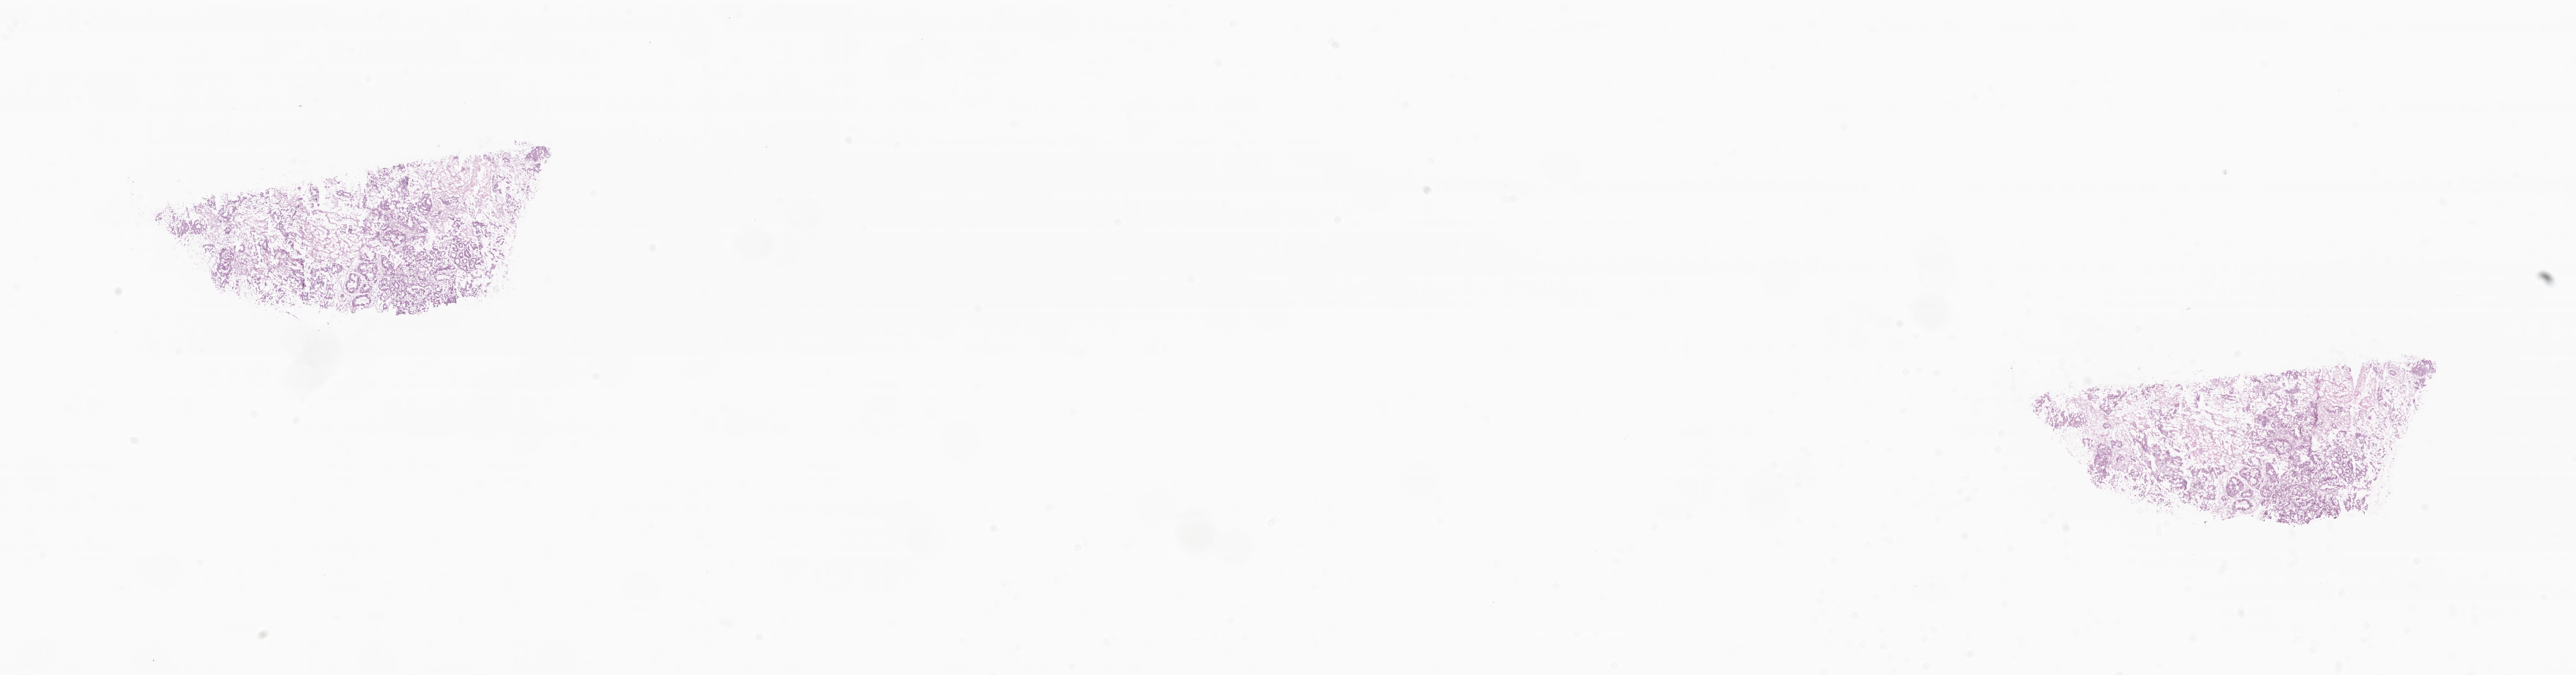
Whole-slide image, haematoxylin and eosin stain, low-resolution overview of the scanned area, about 34.0 x 8.9 mm, frozen section, primary tumor, anatomic site: rectum. Patient sex: male. Tumor grade: G2 (moderately differentiated). Composition of this section per pathologist review: tumor cells 100%, tumor nuclei 75%, stromal cells 0%, necrosis 0%, normal cells 0%. Infiltration values recorded for this section: lymphocyte infiltration 0%, monocyte infiltration 0%, neutrophil infiltration 0%.
- histologic diagnosis: Adenocarcinoma, NOS
- AJCC pathologic stage: Stage IIA
- section: bottom of the tissue portion